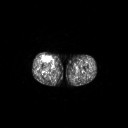
FDG PET of an extremity soft-tissue mass (from a PET/CT study), one axial slice. Slice 260 of 311 in the series (ordered by position). 128 × 128 image matrix, field of view 700 × 700 mm. Male patient, age 56 years. Case-level facts recorded for this patient, not image findings: histological type: pleiomorphic leiomyosarcoma; grade: intermediate; site of the primary tumour: right thigh.
Structures marked on this image (expert contour drawn on MRI and transferred to this co-registered scan by the dataset authors):
- gross tumour volume including surrounding oedema: bounding box <41,55,51,62> (left, top, right, bottom; pixels)